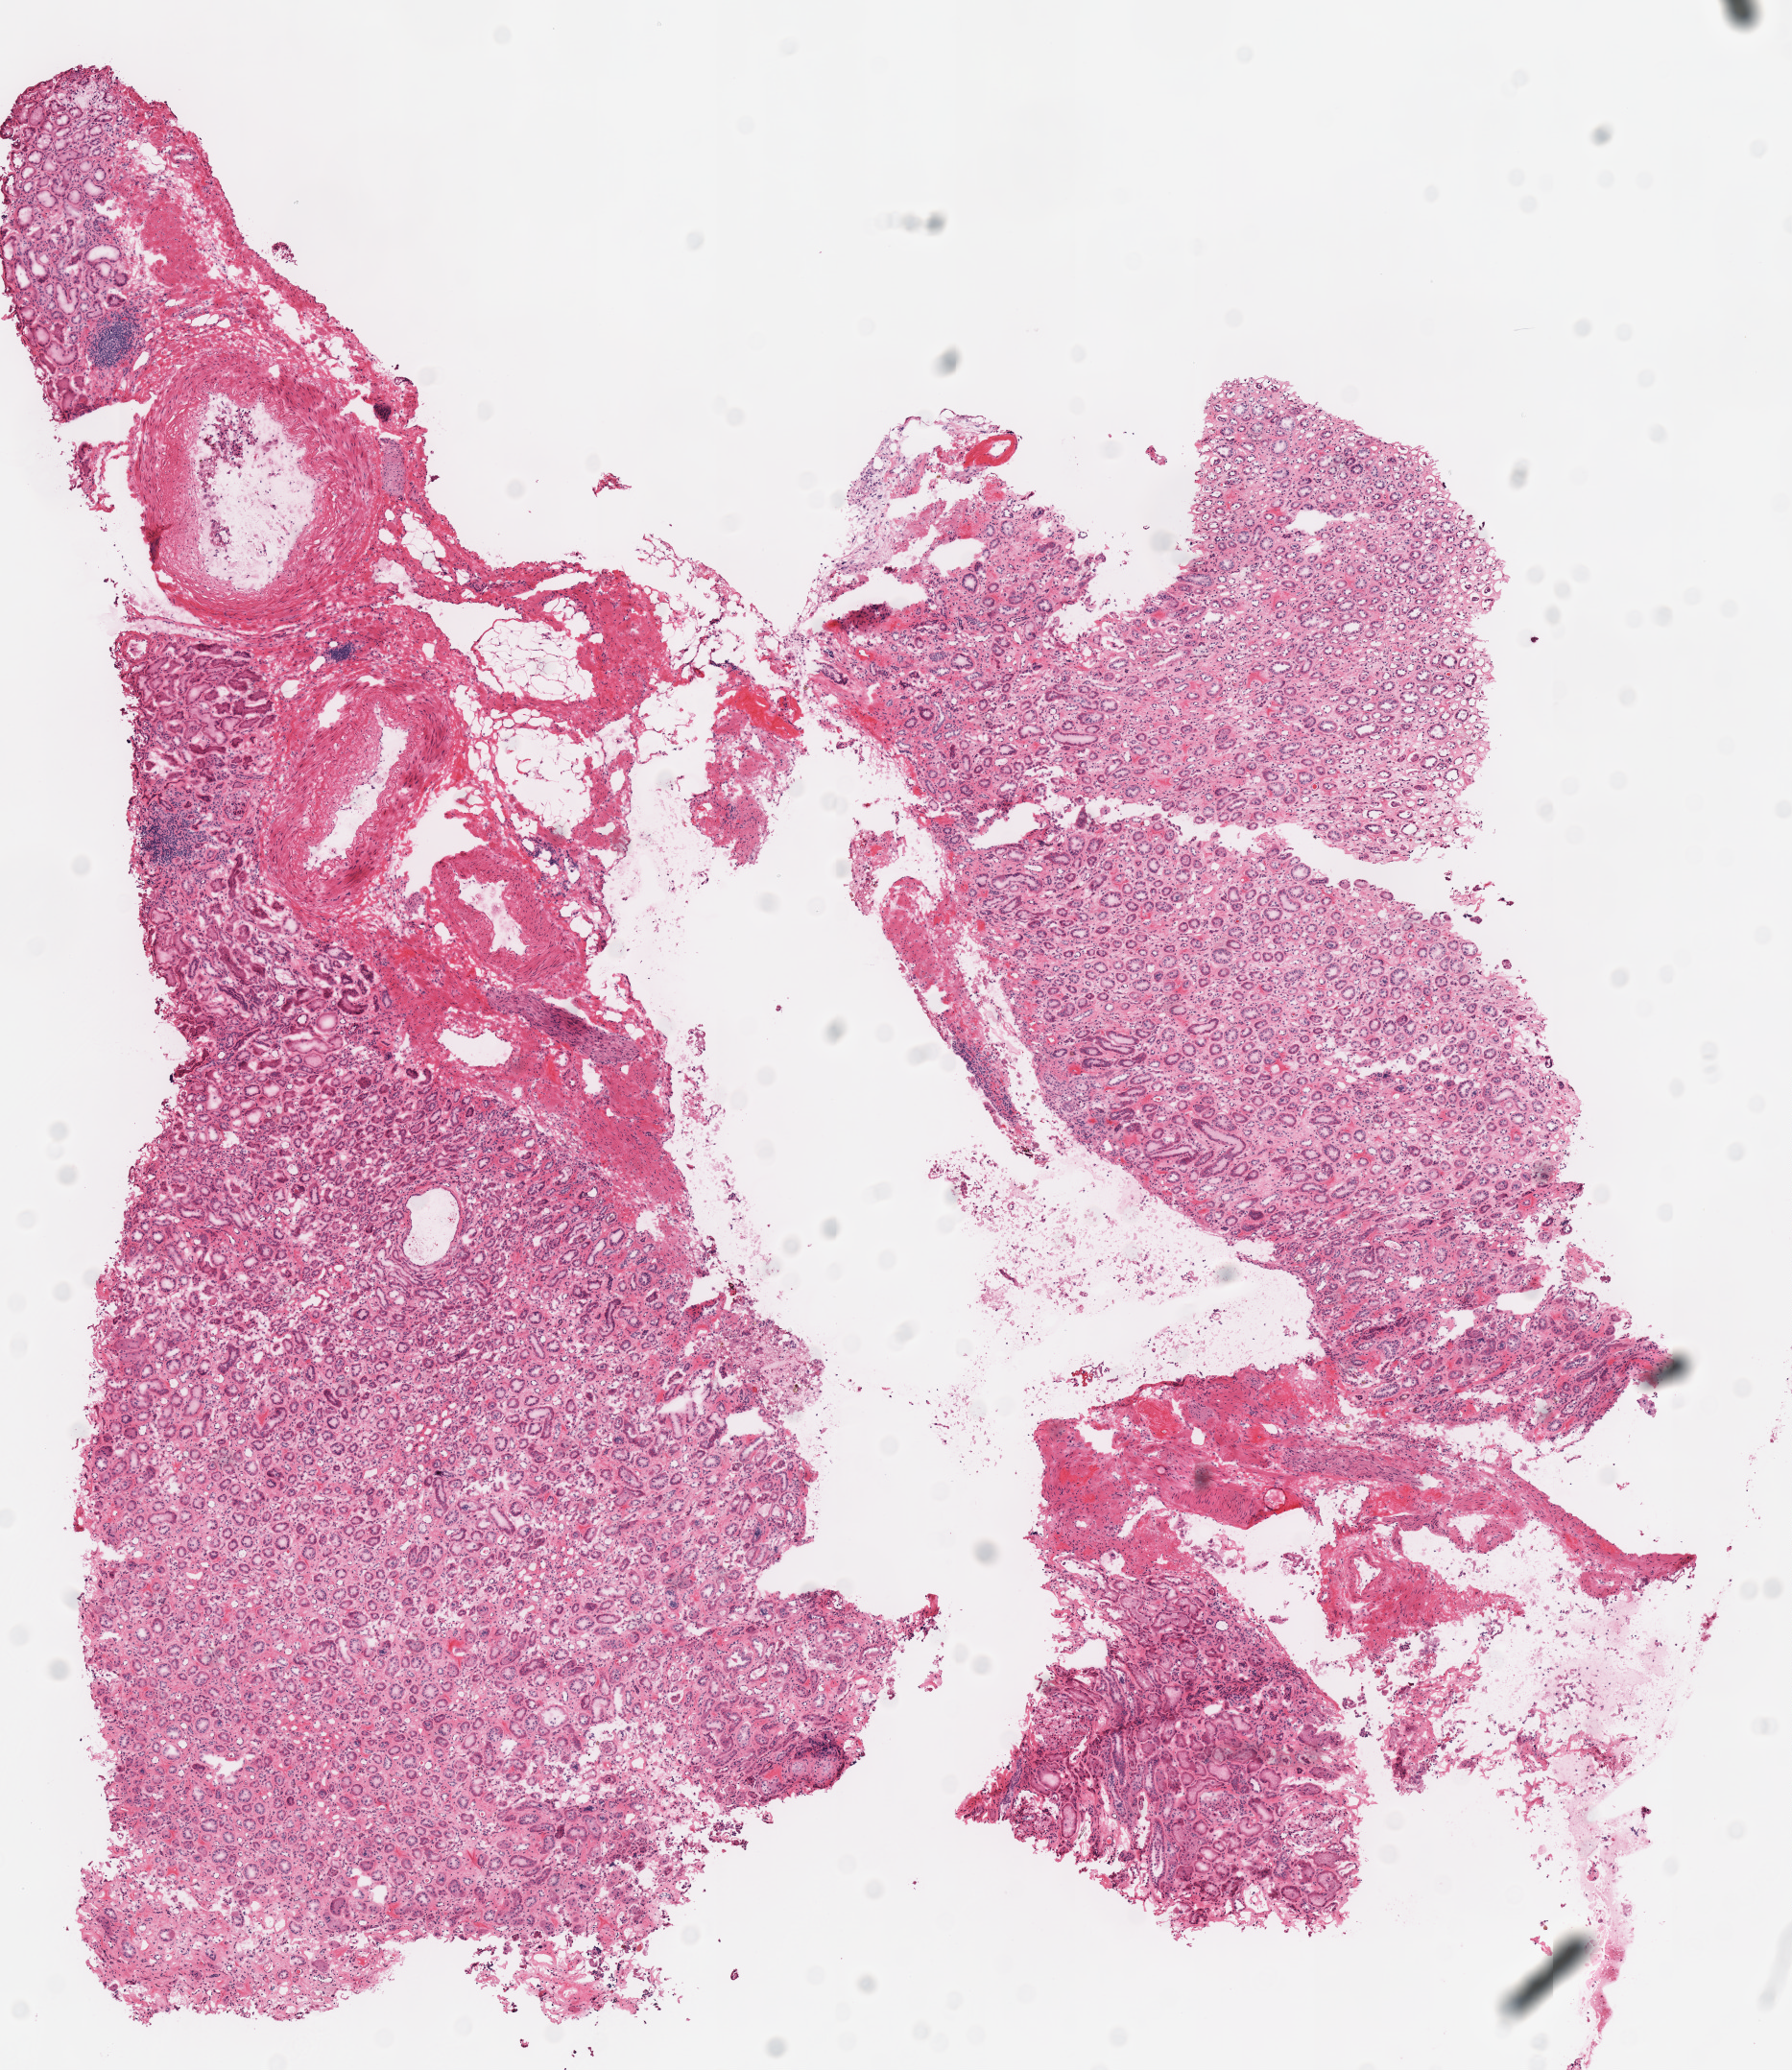
Digitized H&E tissue section (whole slide) — a low-resolution overview of the entire scanned area, about 7.3 x 8.5 mm, frozen section, solid tissue normal (non-tumour tissue) sample from the kidney. Male patient; age at initial diagnosis 72 years.
- this section: solid tissue normal (non-tumour) sample from the same patient
- patient diagnosis: Renal cell carcinoma, chromophobe type